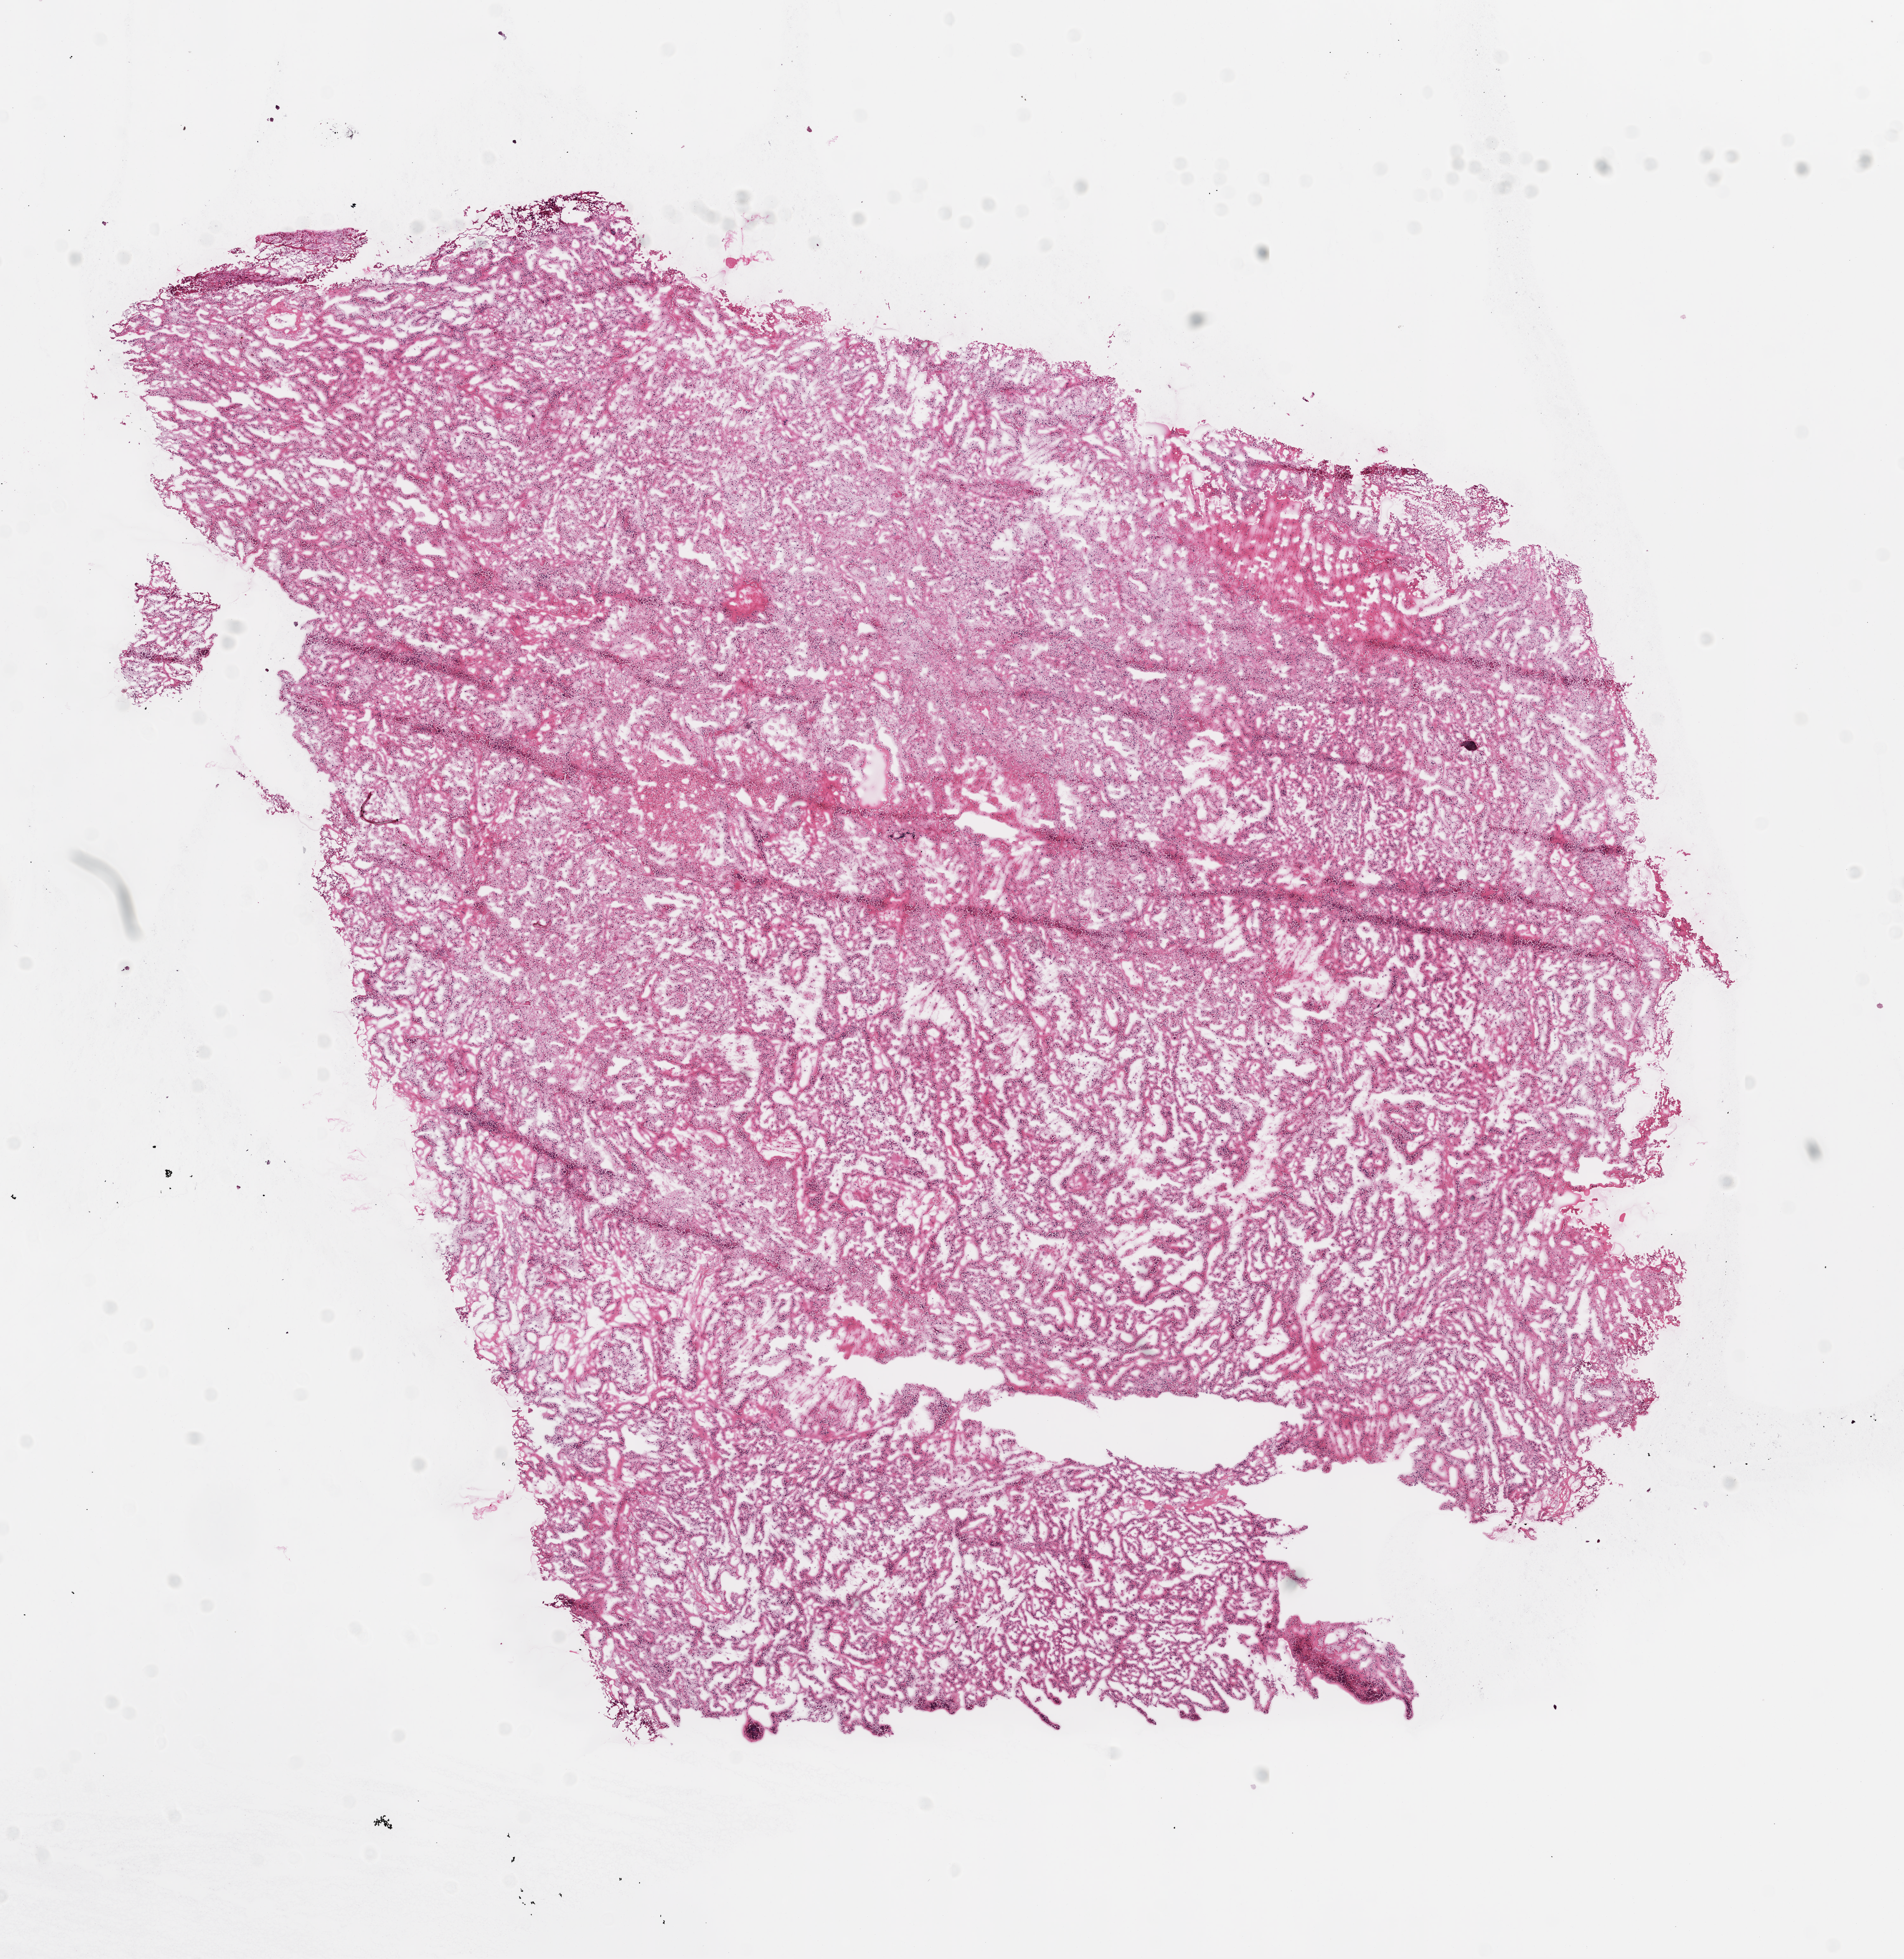
Digitized Hematoxylin and eosin (H&E) stained tissue section (whole slide), a low-resolution overview of the entire scanned area, about 12.0 x 12.4 mm. Frozen section from the top of the tissue portion. Sample: primary tumour, kidney. Male patient; age at initial diagnosis 48 years. Histologic grade: G3 (poorly differentiated). Pathologist review of this section (percent, as recorded): tumour cells 99%, tumour nuclei 80%, normal cells 0%, stromal cells 1%, necrosis 0%.
Histologic diagnosis: Clear cell adenocarcinoma, NOS. Lymph nodes positive (case pathology): 0 of 1 examined. AJCC pathologic stage: II.